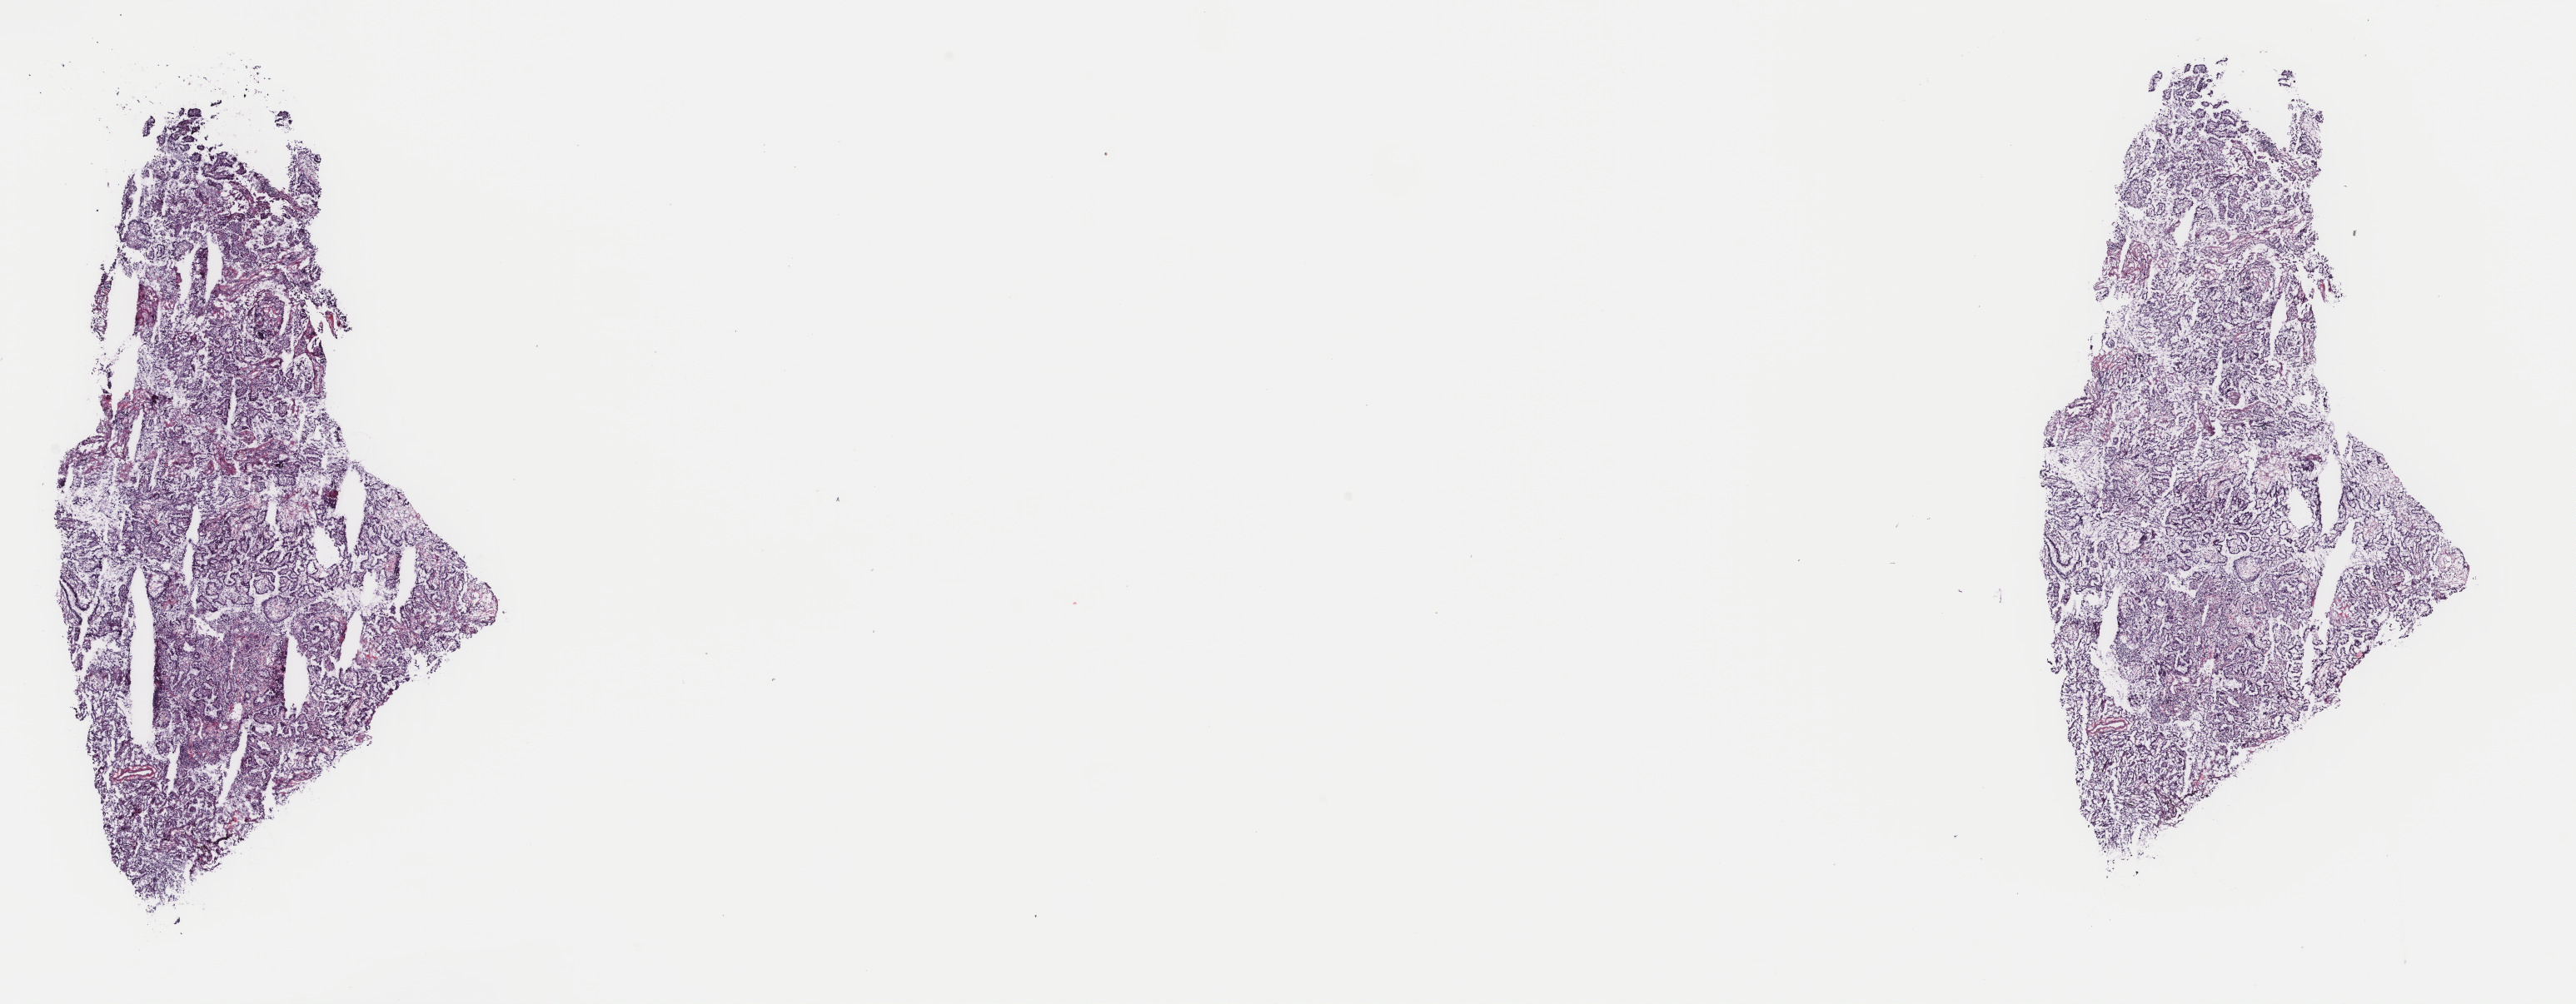
Digitized Hematoxylin and eosin (H&E) stained tissue section (whole slide), a low-resolution overview of the entire scanned area, about 24.6 x 9.6 mm (slide scanned at 40x); frozen section from the top of the tissue portion; primary tumour sample from the lung. Male, age 65 years at initial diagnosis. Slide review estimates, as recorded: tumour cells 100%, tumour nuclei 70%, normal cells 0%, stromal cells 0%, necrosis 0%. Inflammatory infiltration, as recorded: lymphocyte infiltration 0%, monocyte infiltration 0%, neutrophil infiltration 0%.
AJCC pathologic stage: IB (6th edition). Histologic diagnosis: Adenocarcinoma with mixed subtypes (upper lobe, lung).